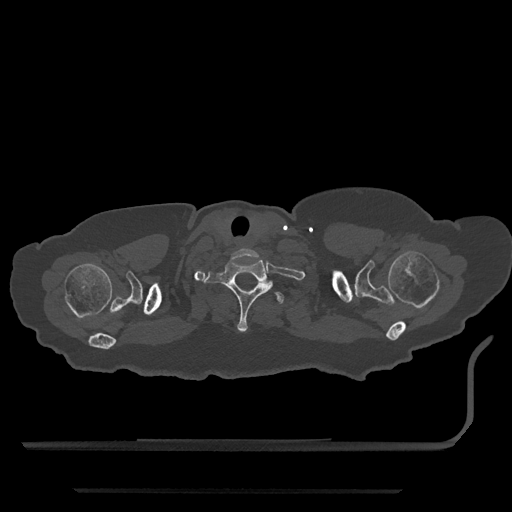
CT including the spine, one axial slice; slice 709 of 797 in the series (ordered by position); reconstruction kernel Br40s/3; 120 kVp; bone window (W 1800 / L 400 HU); 0.5 mm slice thickness; 512 × 512 image matrix, field of view 440 × 440 mm. Female patient, age 51 years. From the clinical record (not read from this slice): primary cancer: neuro; vertebrae with lytic lesions (as recorded): T8.
Structures marked on this image (semi-automatically segmented with operator editing):
- T1 vertebra: bounding box (x1, y1, x2, y2) in pixels: (205, 259, 273, 333)
- T2 vertebra: (256, 281, 284, 304)